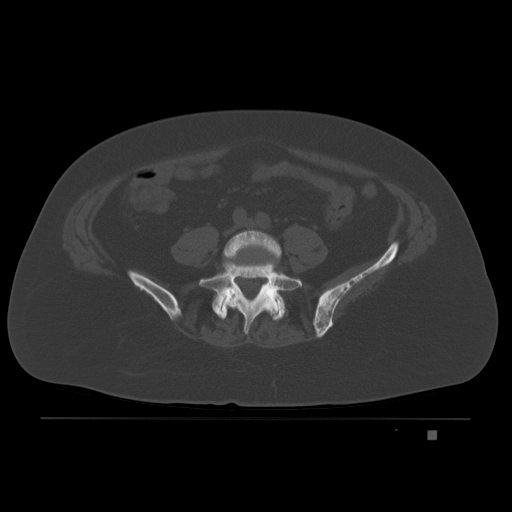
CT including the spine, one axial slice; slice 33 of 221 in the series (ordered by position); bone window (W 1800 / L 400 HU); 512 × 512 image matrix. Patient: female, 63 years. Case-level facts recorded for this patient, not image findings: primary cancer: breast.
Structures marked on this image (semi-automatic segmentation, software-assisted and operator-edited):
- L4 vertebra: bounding box [x1, y1, x2, y2] px = [220, 230, 282, 285]
- L5 vertebra: [199, 260, 299, 334]